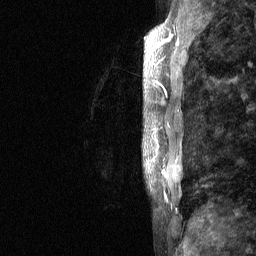
Breast MRI (dynamic contrast-enhanced), one sagittal slice; position 16 of 64 along the scan axis; dynamic contrast-enhanced study with each time point stored as its own series, time point 2 of 3 at this slice position (early post-contrast, ordered by acquisition time); 1.5 T; TE 4.8 ms, TR 27 ms; 2 mm slice thickness; 256 × 256 image matrix. Patient: female, 36 years. Case-level facts recorded for this patient, not image findings: setting: breast cancer imaged before/during neoadjuvant chemotherapy; receptor status: HR-positive, HER2-negative.
Outlined on this slice (semi-automatic segmentation, software-assisted and operator-edited):
- analysis volume of interest (the breast-tissue region the enhancement analysis was run in; not a lesion): bounding box [x1, y1, x2, y2] px = [142, 12, 208, 237]
- tumour enhancement mask (voxels above the 90 % enhancement threshold inside the analysis volume of interest): [152, 35, 179, 84]